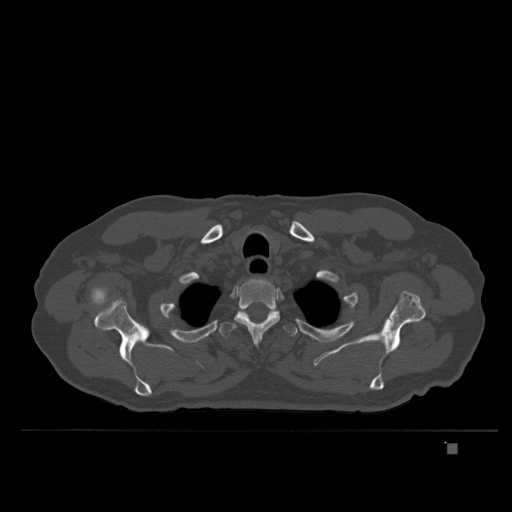
CT including the spine, one axial slice; slice 310 of 435 in the series (ordered by position); bone window (W 1800 / L 400 HU); 512 × 512 image matrix, field of view 434 × 434 mm. Male patient, age 73 years. From the clinical record (not read from this slice): primary cancer: skin.
Outlined on this slice (semi-automatic segmentation, software-assisted and operator-edited):
- T2 vertebra: bounding box [x1, y1, x2, y2] px = [234, 279, 280, 344]
- T3 vertebra: [219, 311, 298, 338]